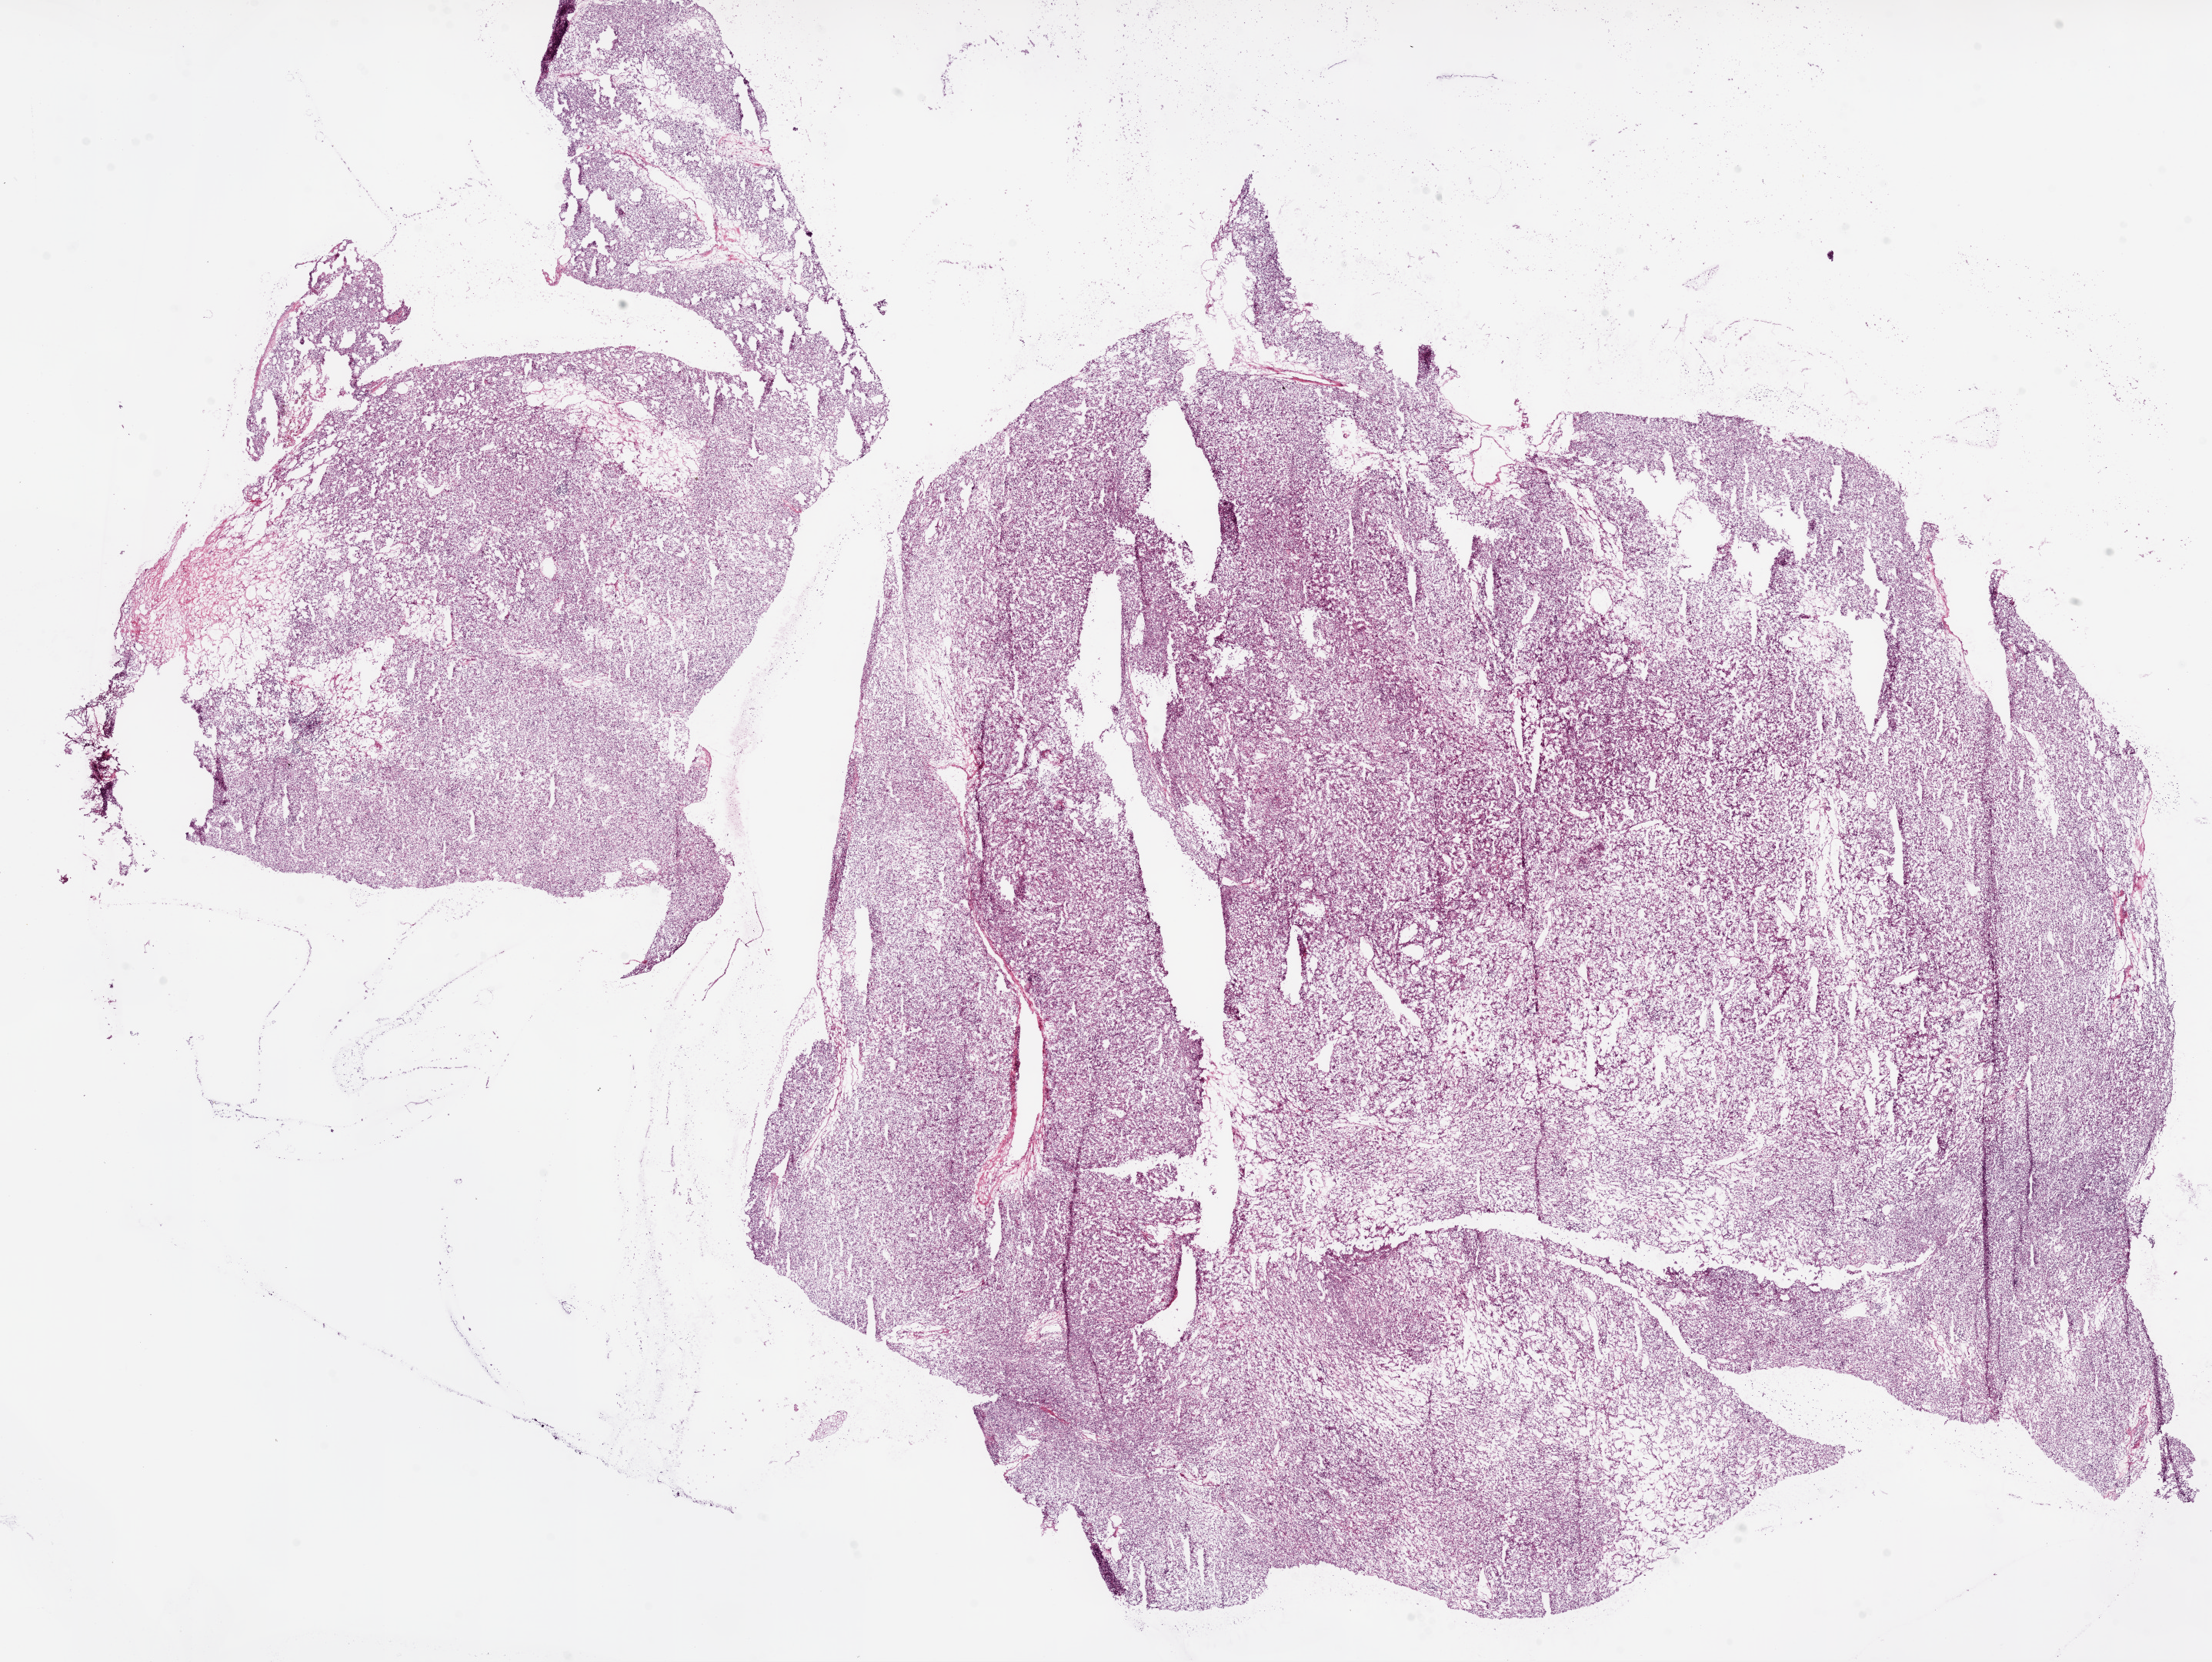
H&E whole-slide image, whole scanned area (about 23.1 x 17.3 mm, slide scanned at 20x) shown as a low-resolution overview. Frozen section from the bottom of the tissue portion. Kidney, primary tumour sample. Female, age 68 years at initial diagnosis. Histologic grade: G3 (poorly differentiated). Composition of this section per pathologist review: tumour cells 90%, tumour nuclei 90%, normal cells 0%, stromal cells 10%, necrosis 0%.
AJCC pathologic stage: II. Histologic diagnosis: Clear cell adenocarcinoma, NOS. Laterality: right.